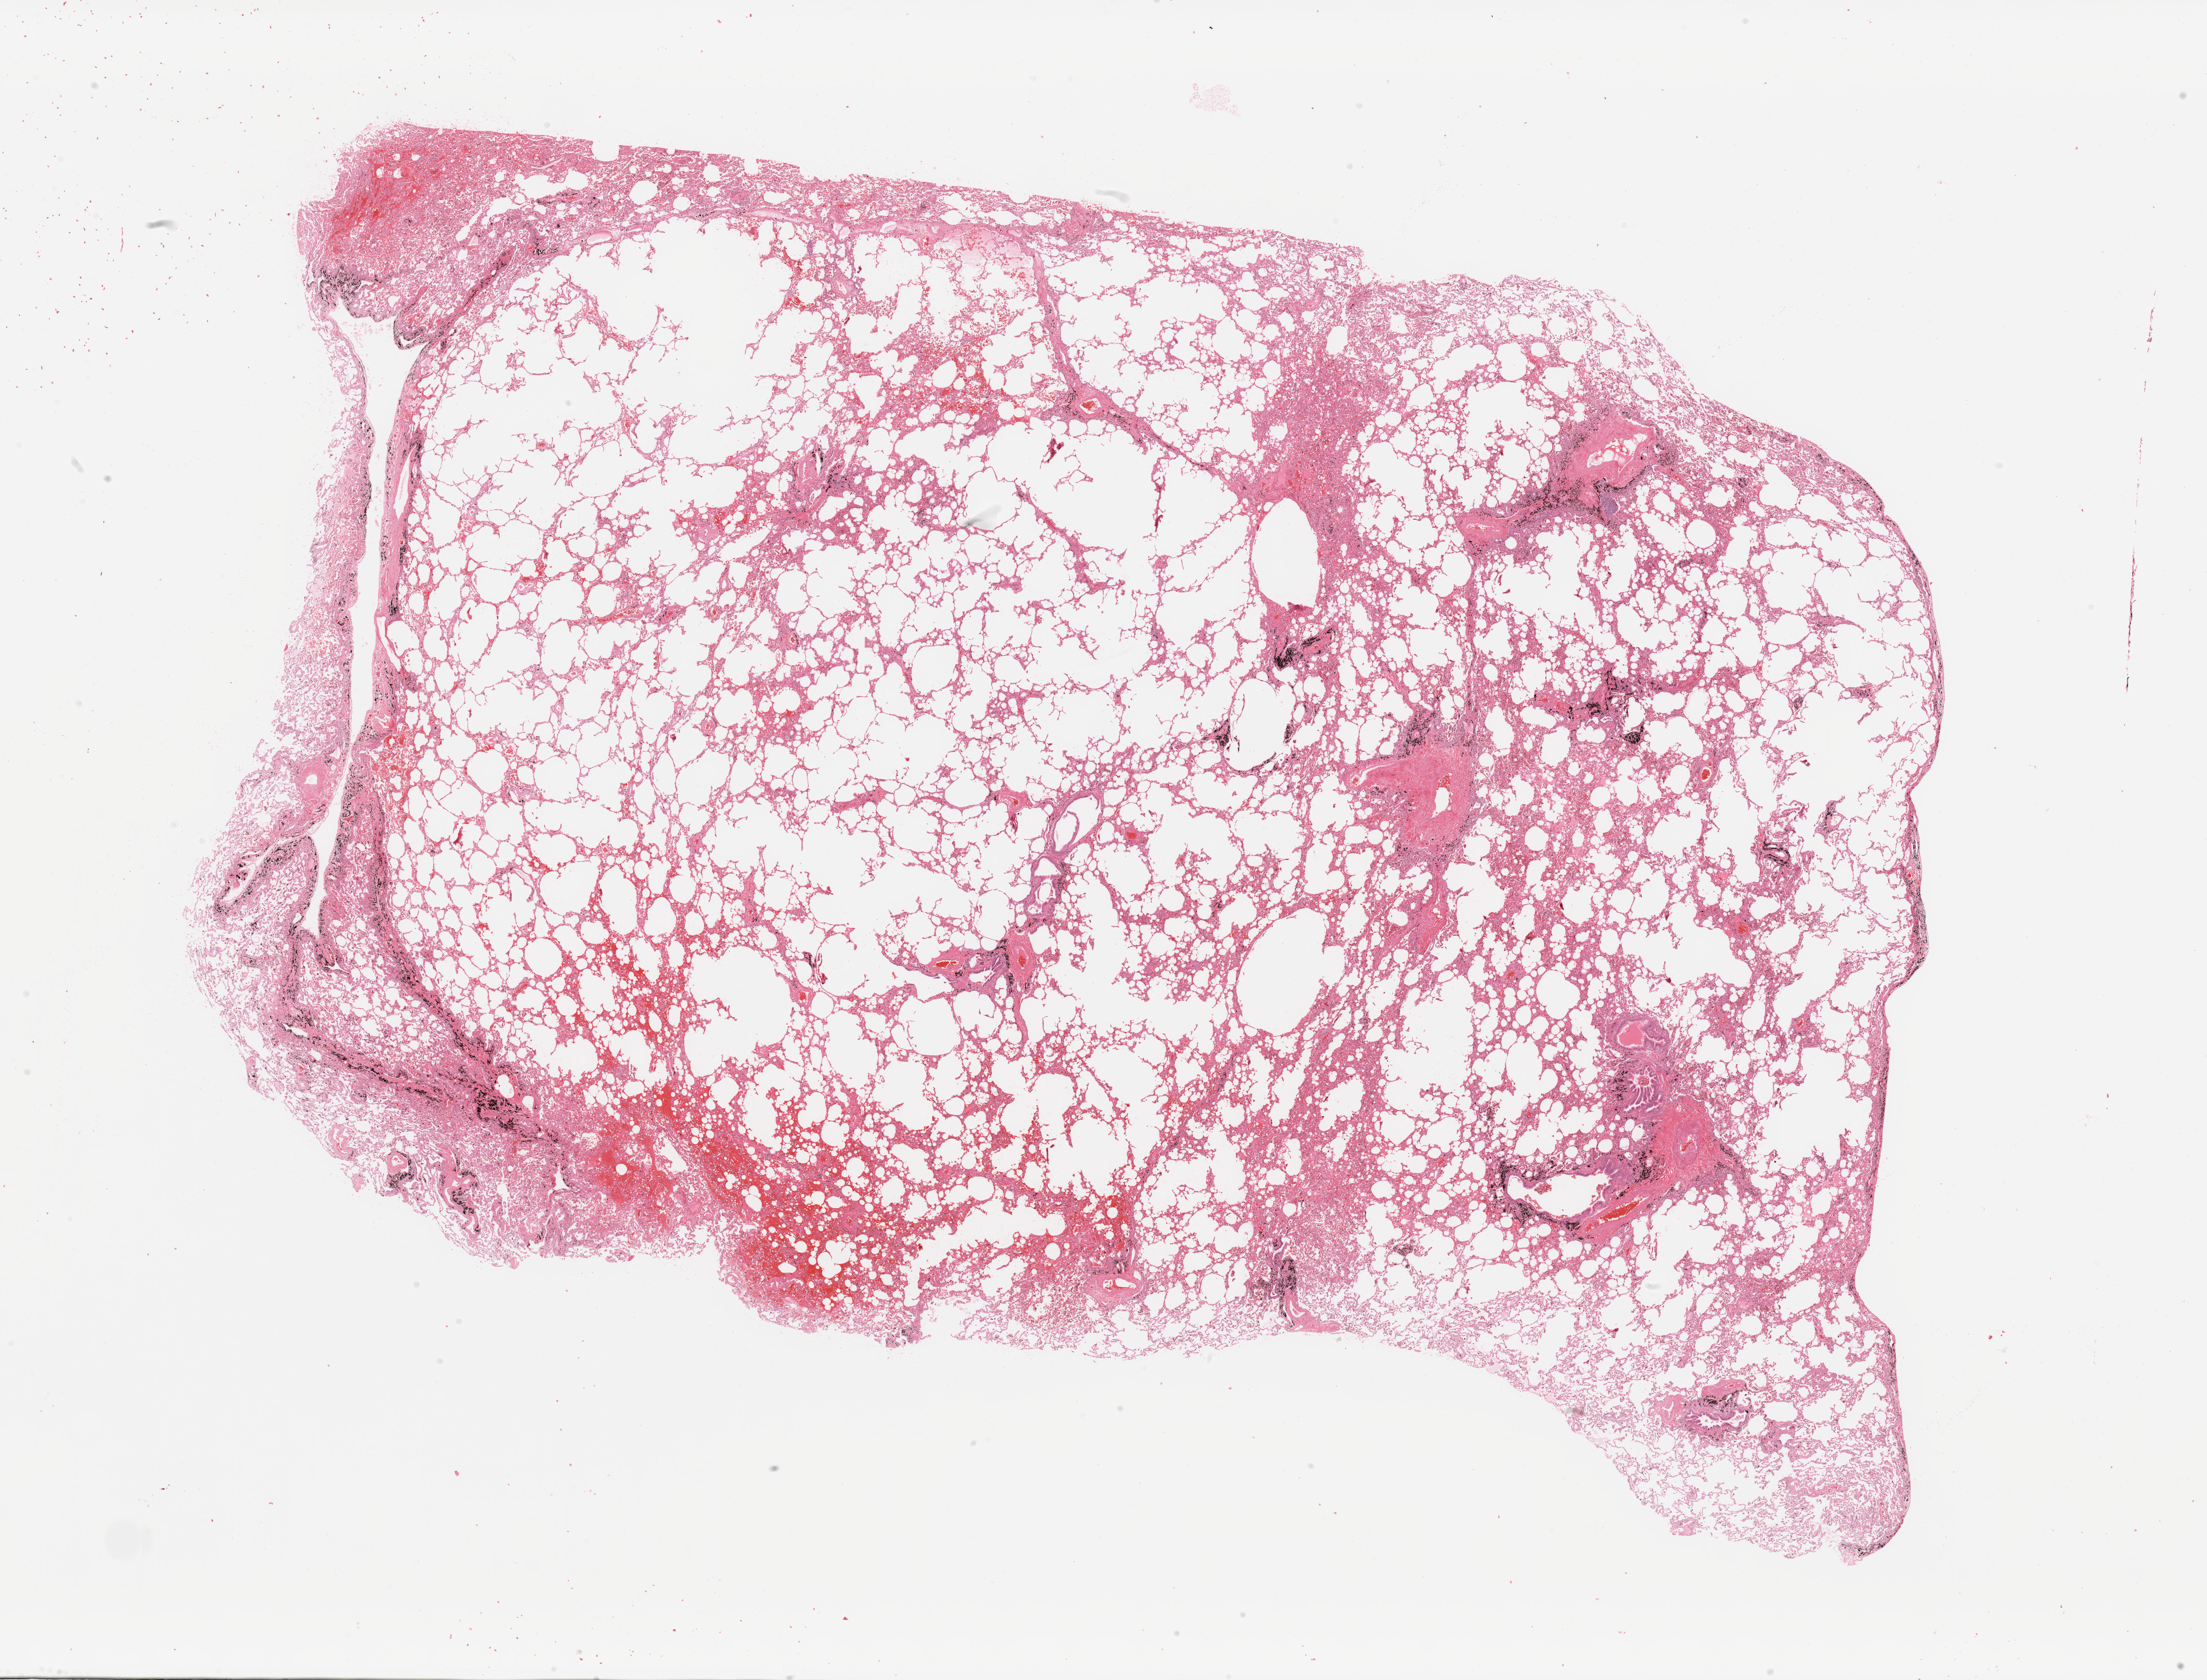
H&E-stained whole-slide image, low-resolution overview of the scanned area, about 30.5 x 23.2 mm (acquisition: 20x scan). Normal (non-tumour) tissue sample, sampled site: lung. 60-year-old male patient.
• this section: normal (non-tumour) tissue from the same patient
• patient diagnosis: Adenocarcinoma, NOS